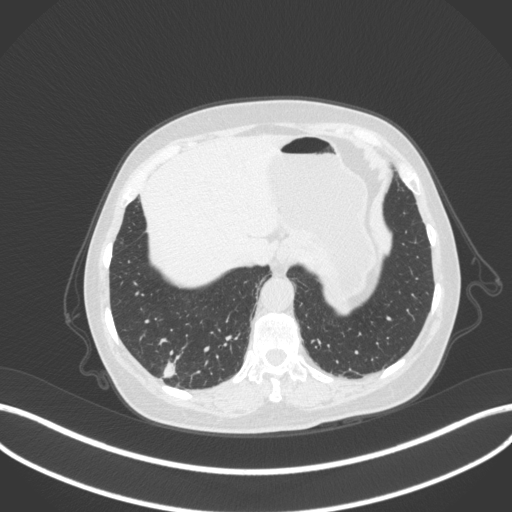
Chest CT, one axial slice. Slice 48 of 340 in the series (ordered by position). Reconstruction kernel B31f. Lung window (W 1500 / L -600 HU). 512 × 512 image matrix. Patient: female, 69 years. Case-level facts recorded for this patient, not image findings: clinical TNM (as recorded): T1b N0 M0.
Structures marked on this image (bounding box drawn by a radiologist):
- lung tumour (recorded histology: adenocarcinoma): bounding box [x1, y1, x2, y2] px = [160, 357, 181, 386]